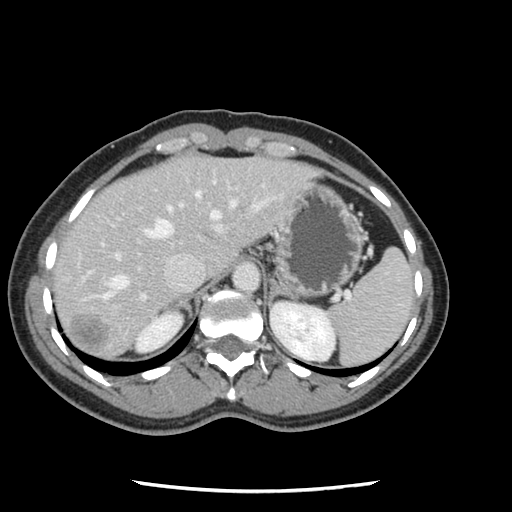
Contrast-enhanced abdominal CT, one axial slice; position 91 of 134 along the scan axis; 120 kVp; intravenous contrast given; soft-tissue window (W 400 / L 40 HU); 512 × 512 image matrix. Female patient, age 43 years. From the clinical record (not read from this slice): diagnosis: colorectal cancer liver metastases, imaged before liver resection; multiple liver metastases: yes; largest metastasis: 3.4 cm; disease in both lobes: yes.
Structures marked on this image (outlined manually by an expert reader):
- hepatic veins: bounding box [x1, y1, x2, y2] px = [102, 191, 266, 300]
- liver: [55, 156, 314, 360]
- planned liver remnant (the part of the liver to remain after resection): [54, 160, 192, 309]
- portal vein (with intrahepatic branches): [63, 179, 230, 311]
- liver metastasis: [71, 314, 111, 354]